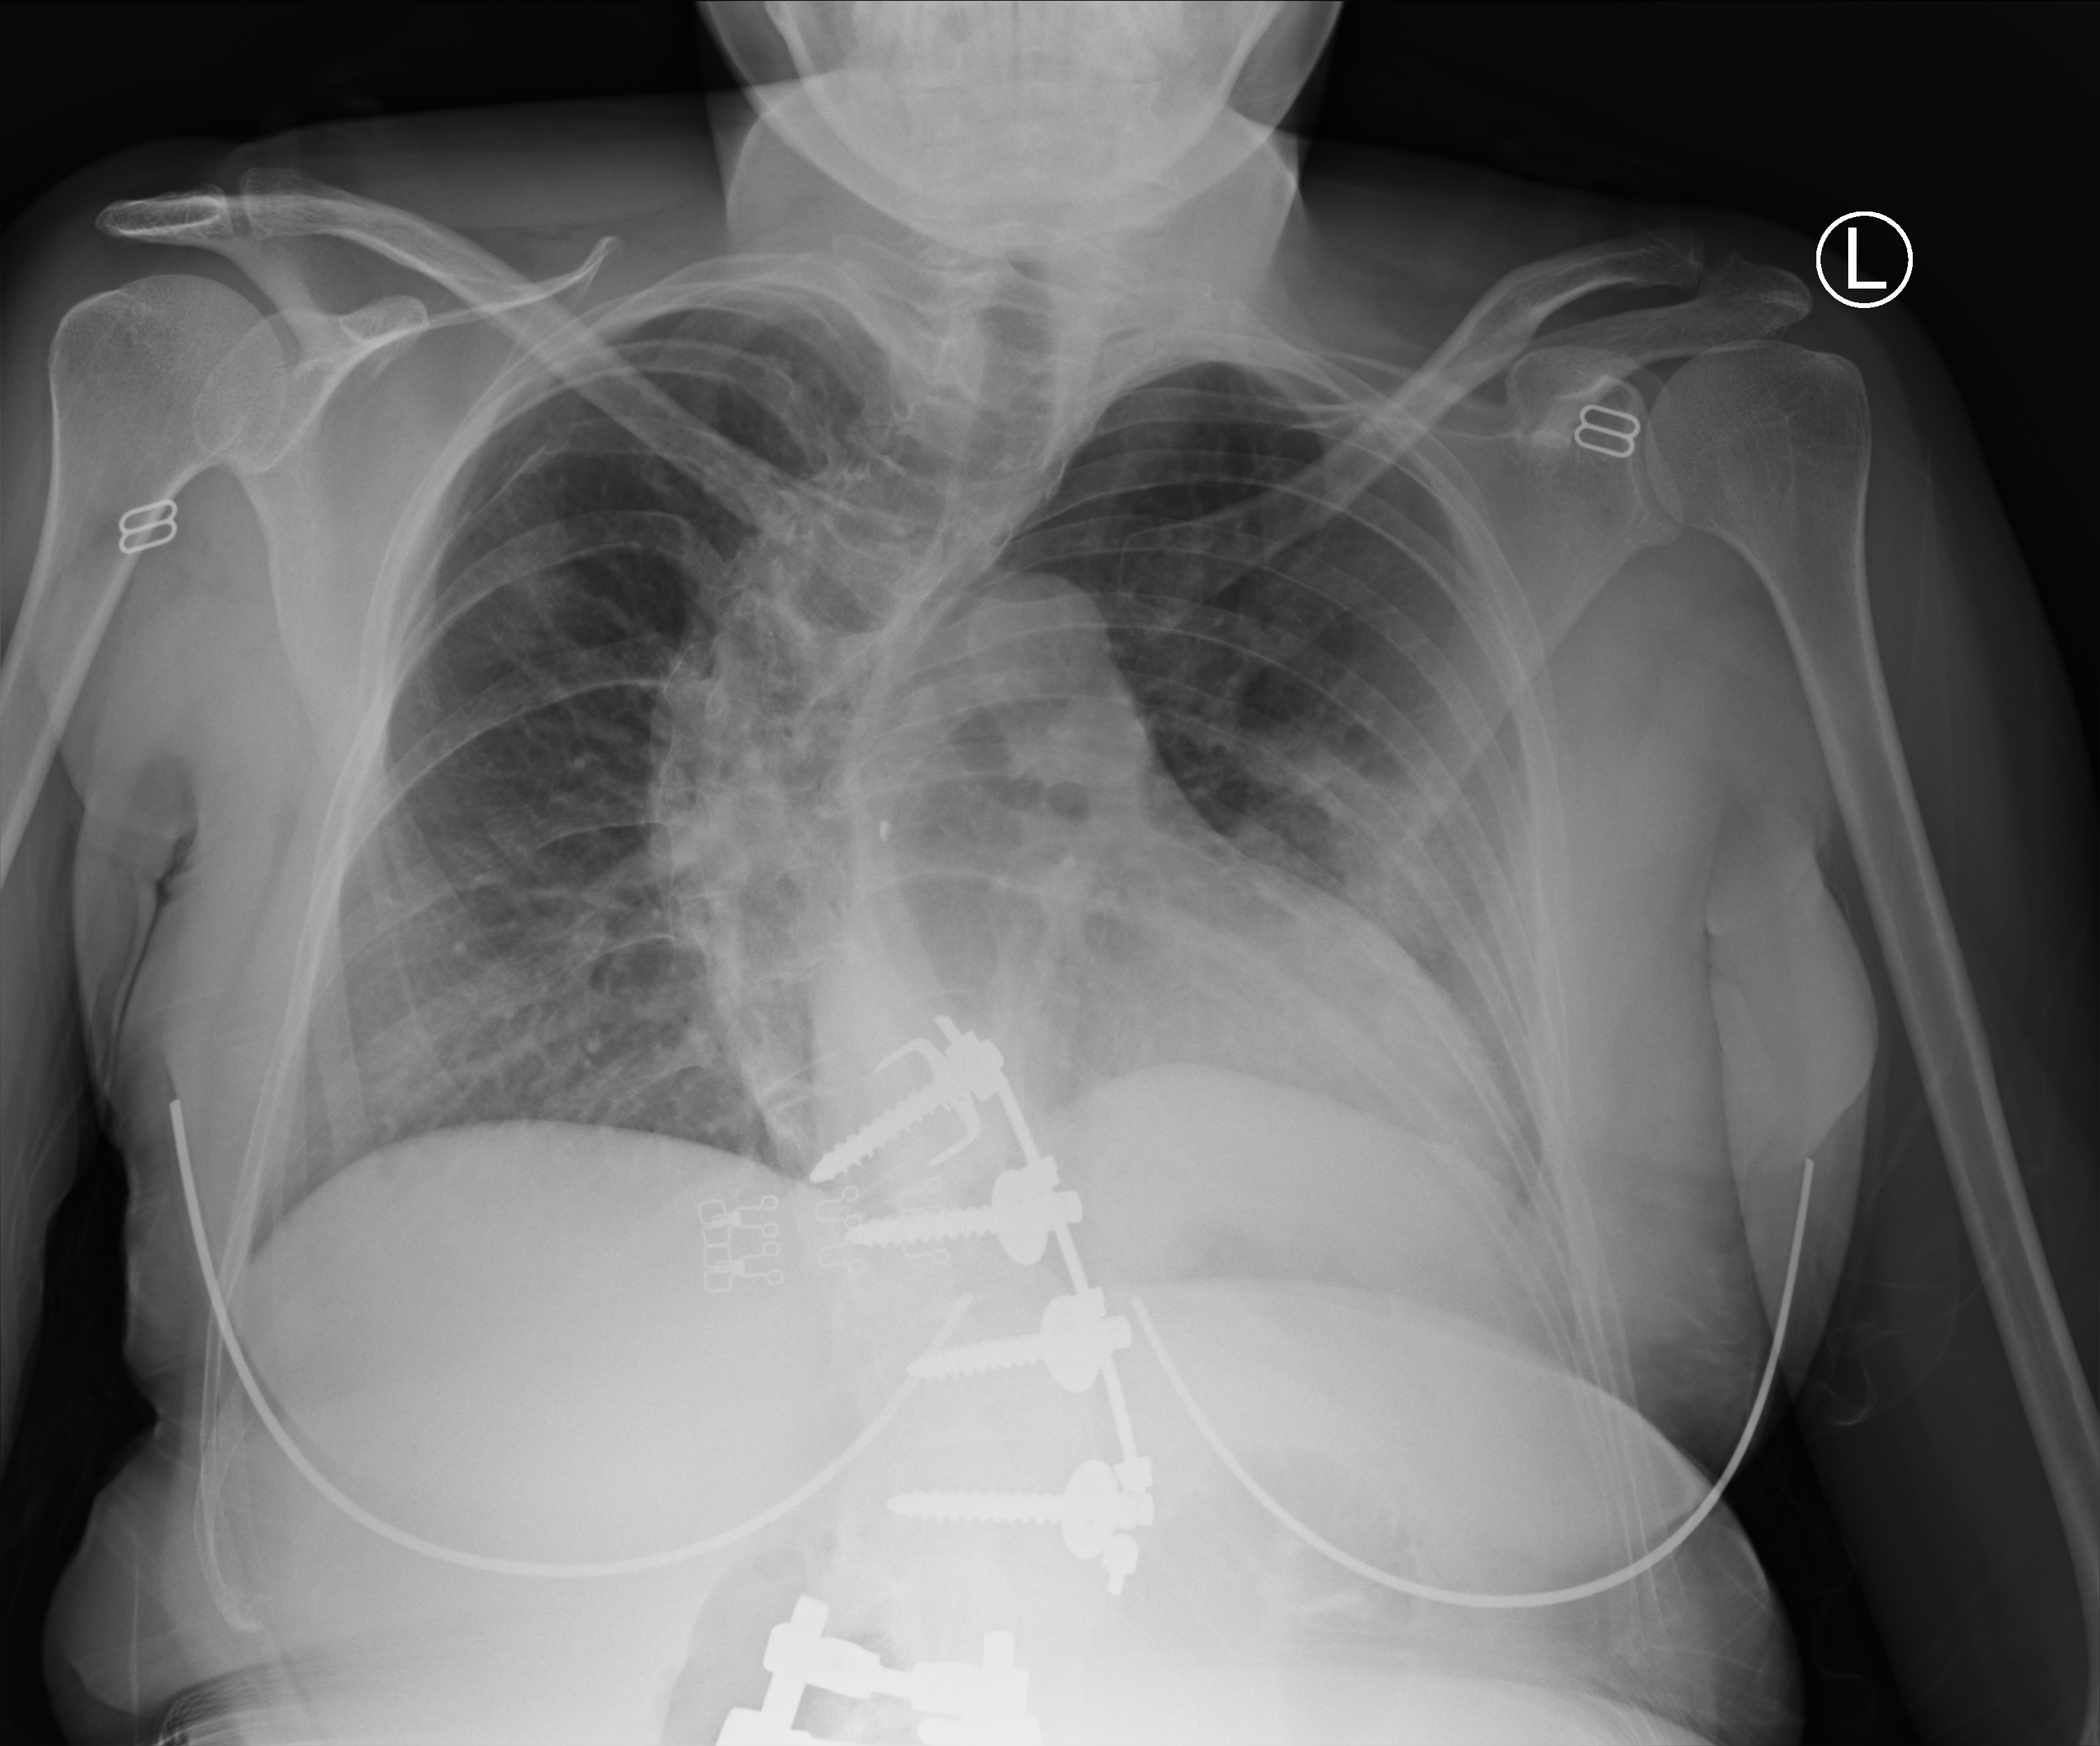
Bedside chest radiograph (computed radiography); anteroposterior (AP) projection. Female patient hospitalised with COVID-19, age 18–59 years.
From the hospital-stay record, not from the radiograph (when in the stay this image was taken is not recorded): mechanically ventilated during this hospital stay: no; COPD (admission record): no; smoking status (admission record): former.